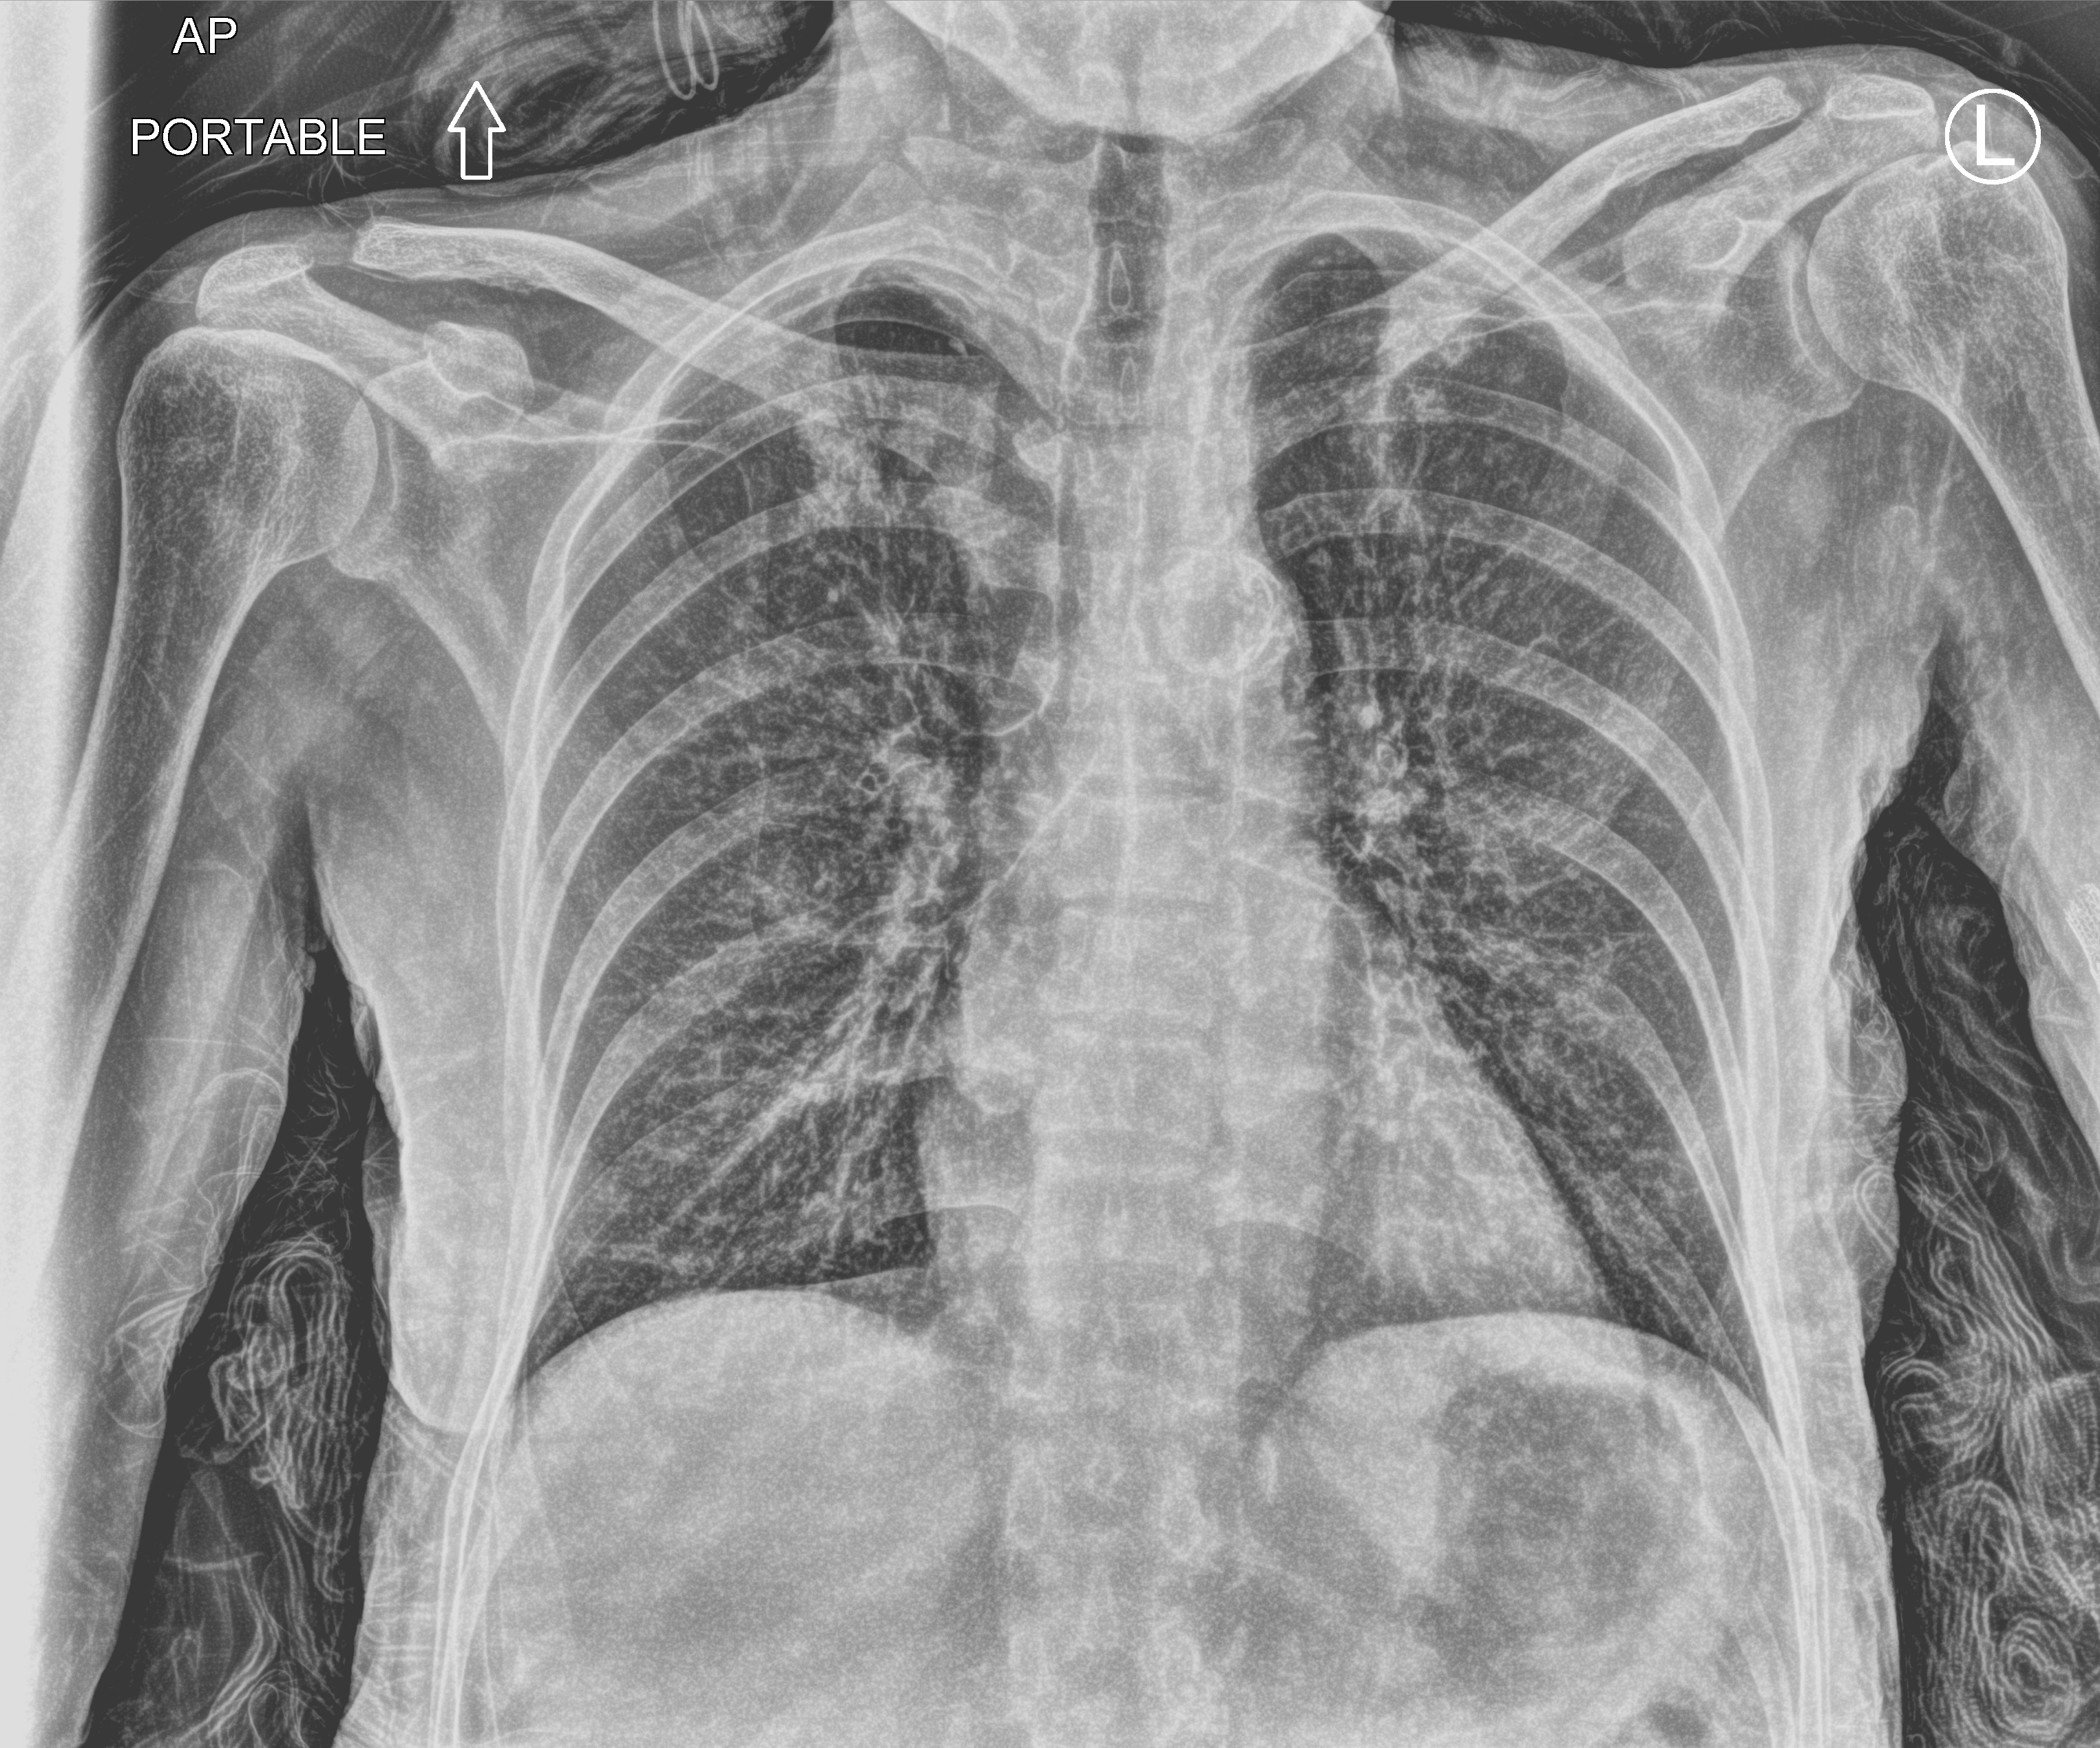
Chest X-ray (portable); anteroposterior (AP) projection. Patient hospitalised with COVID-19; female, aged 18–59 years.
Hospital-stay facts (about this admission, not read from this image; timing relative to this image not recorded): length of hospital stay: 7 days.